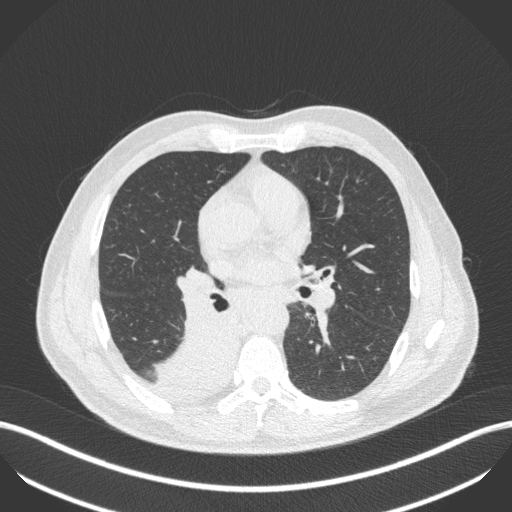
Chest CT, one axial slice; 100 kVp; lung window (W 1500 / L -600 HU); 1 mm slice thickness; 512 × 512 image matrix, field of view 400 × 400 mm. Patient: male, 61 years. From the clinical record (not read from this slice): clinical TNM (as recorded): T1 N0 M0; histopathological grade: G3.
Annotated regions visible in this slice (bounding box drawn by a radiologist):
- lung tumour (recorded histology: small cell carcinoma): box from (x=151, y=315) to (x=240, y=407) px